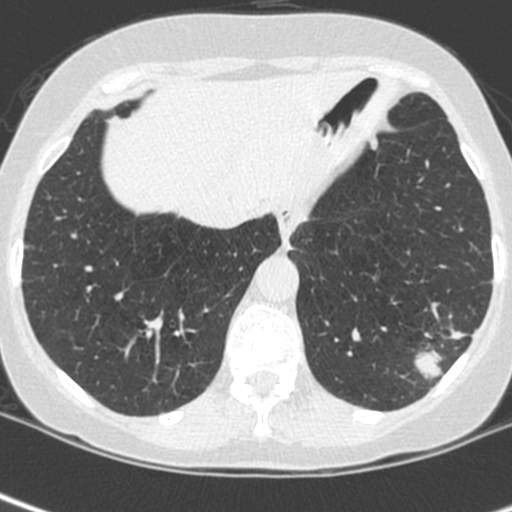
Axial slice from a low-dose chest CT screening exam, first (baseline) screen, lung window (W 1500 / L -600 HU), 1.3 mm slice thickness, standard (soft-tissue) reconstruction kernel (C), slice 184 of 252 in the series, 512 × 512 image matrix. Female participant, aged 56 years at enrolment. Current smoker at enrolment.
• Lesion marked by an expert reader, bounding box [x1, y1, x2, y2] px = [399, 301, 481, 386].
• Reader record for this screening exam (exam-level; its link to the box is not recorded): non-calcified nodule or mass ≥4 mm, left lower lobe, 37 × 29 mm, spiculated (stellate) margins, ground glass attenuation.
• Participant outcome: lung cancer diagnosed 91 days after this screen — squamous cell carcinoma, NOS, left lower lobe, poorly differentiated (G3), stage IIIA (AJCC 6th edition), 35 mm at pathology.